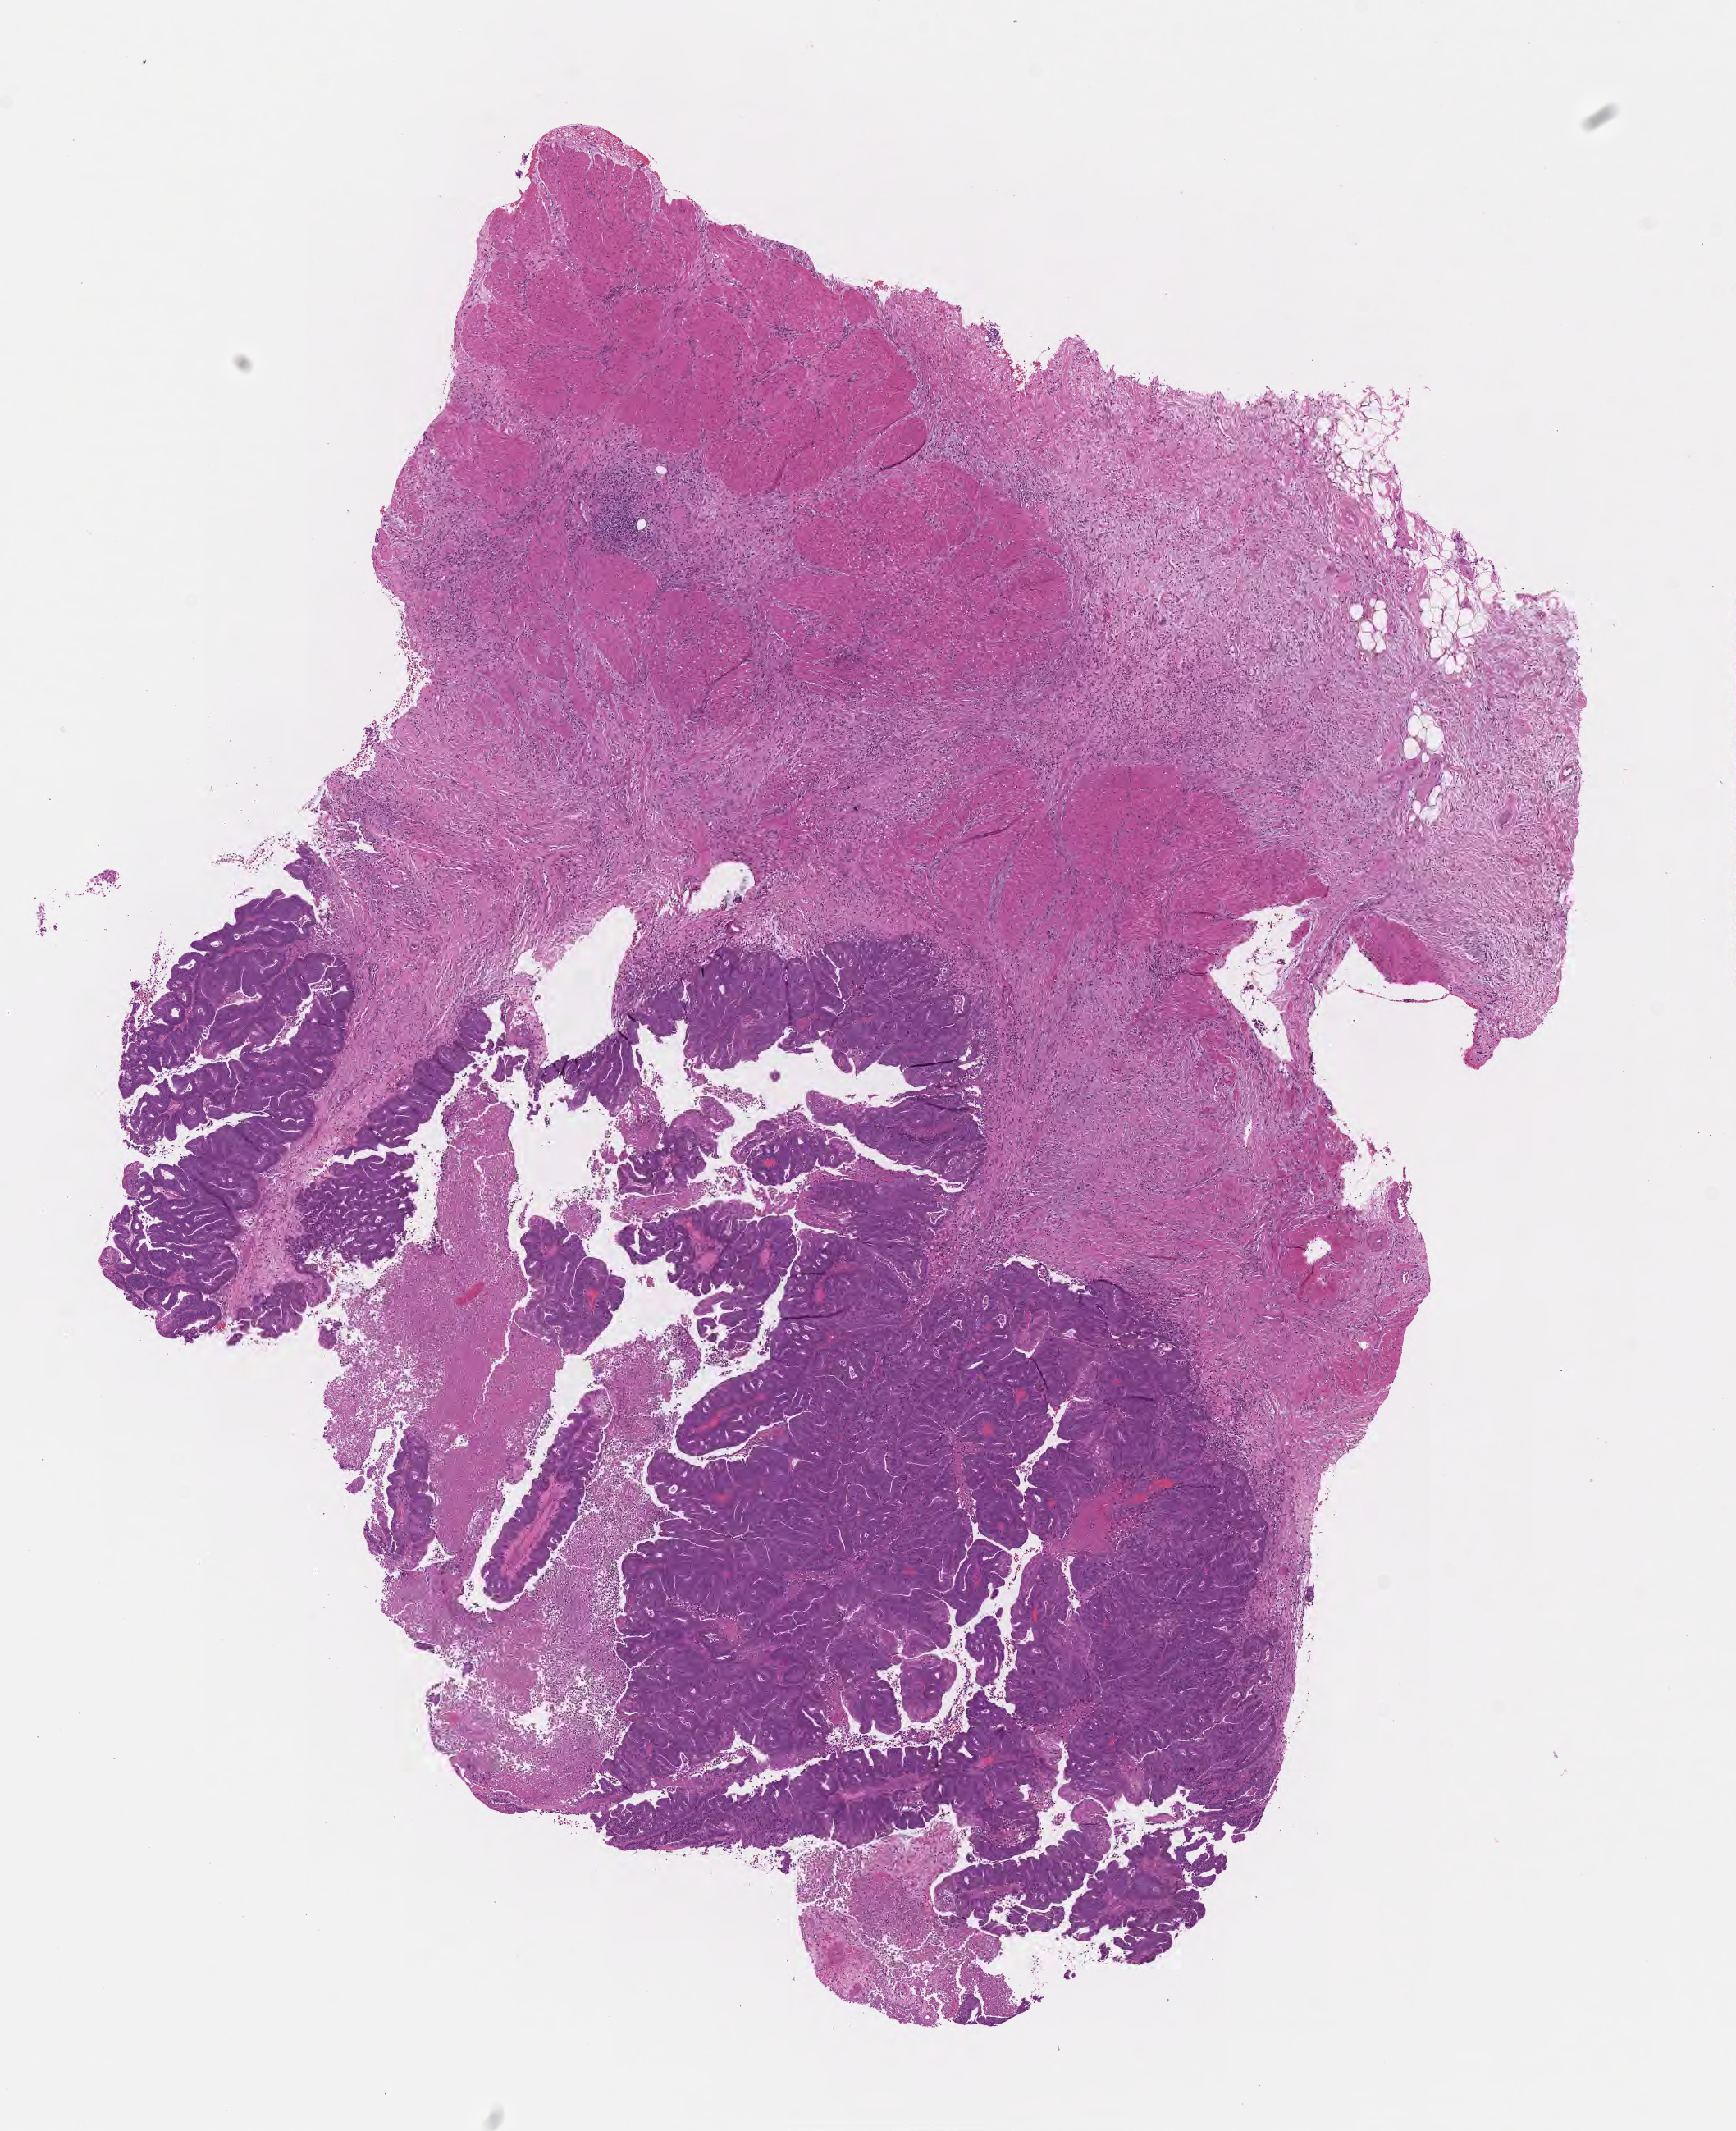
Whole-slide image, hematoxylin and eosin (H&E) stain, shown as a low-resolution overview of the whole scanned area (about 8.6 x 10.5 mm), FFPE section, specimen: primary tumor, site: rectum. Patient: male, age at initial diagnosis 61 years. Tumor grade: G2 (moderately differentiated). Slide review estimates, as recorded: tumor cells 75%, tumor nuclei 75%, stromal cells 20%, necrosis 5%, normal cells 0%. Infiltration values recorded for this section: lymphocyte infiltration 6%, monocyte infiltration 2%, neutrophil infiltration 7%.
Histologic diagnosis: Adenocarcinoma, NOS. AJCC pathologic stage: Stage IIA. Section: bottom of the tissue portion.